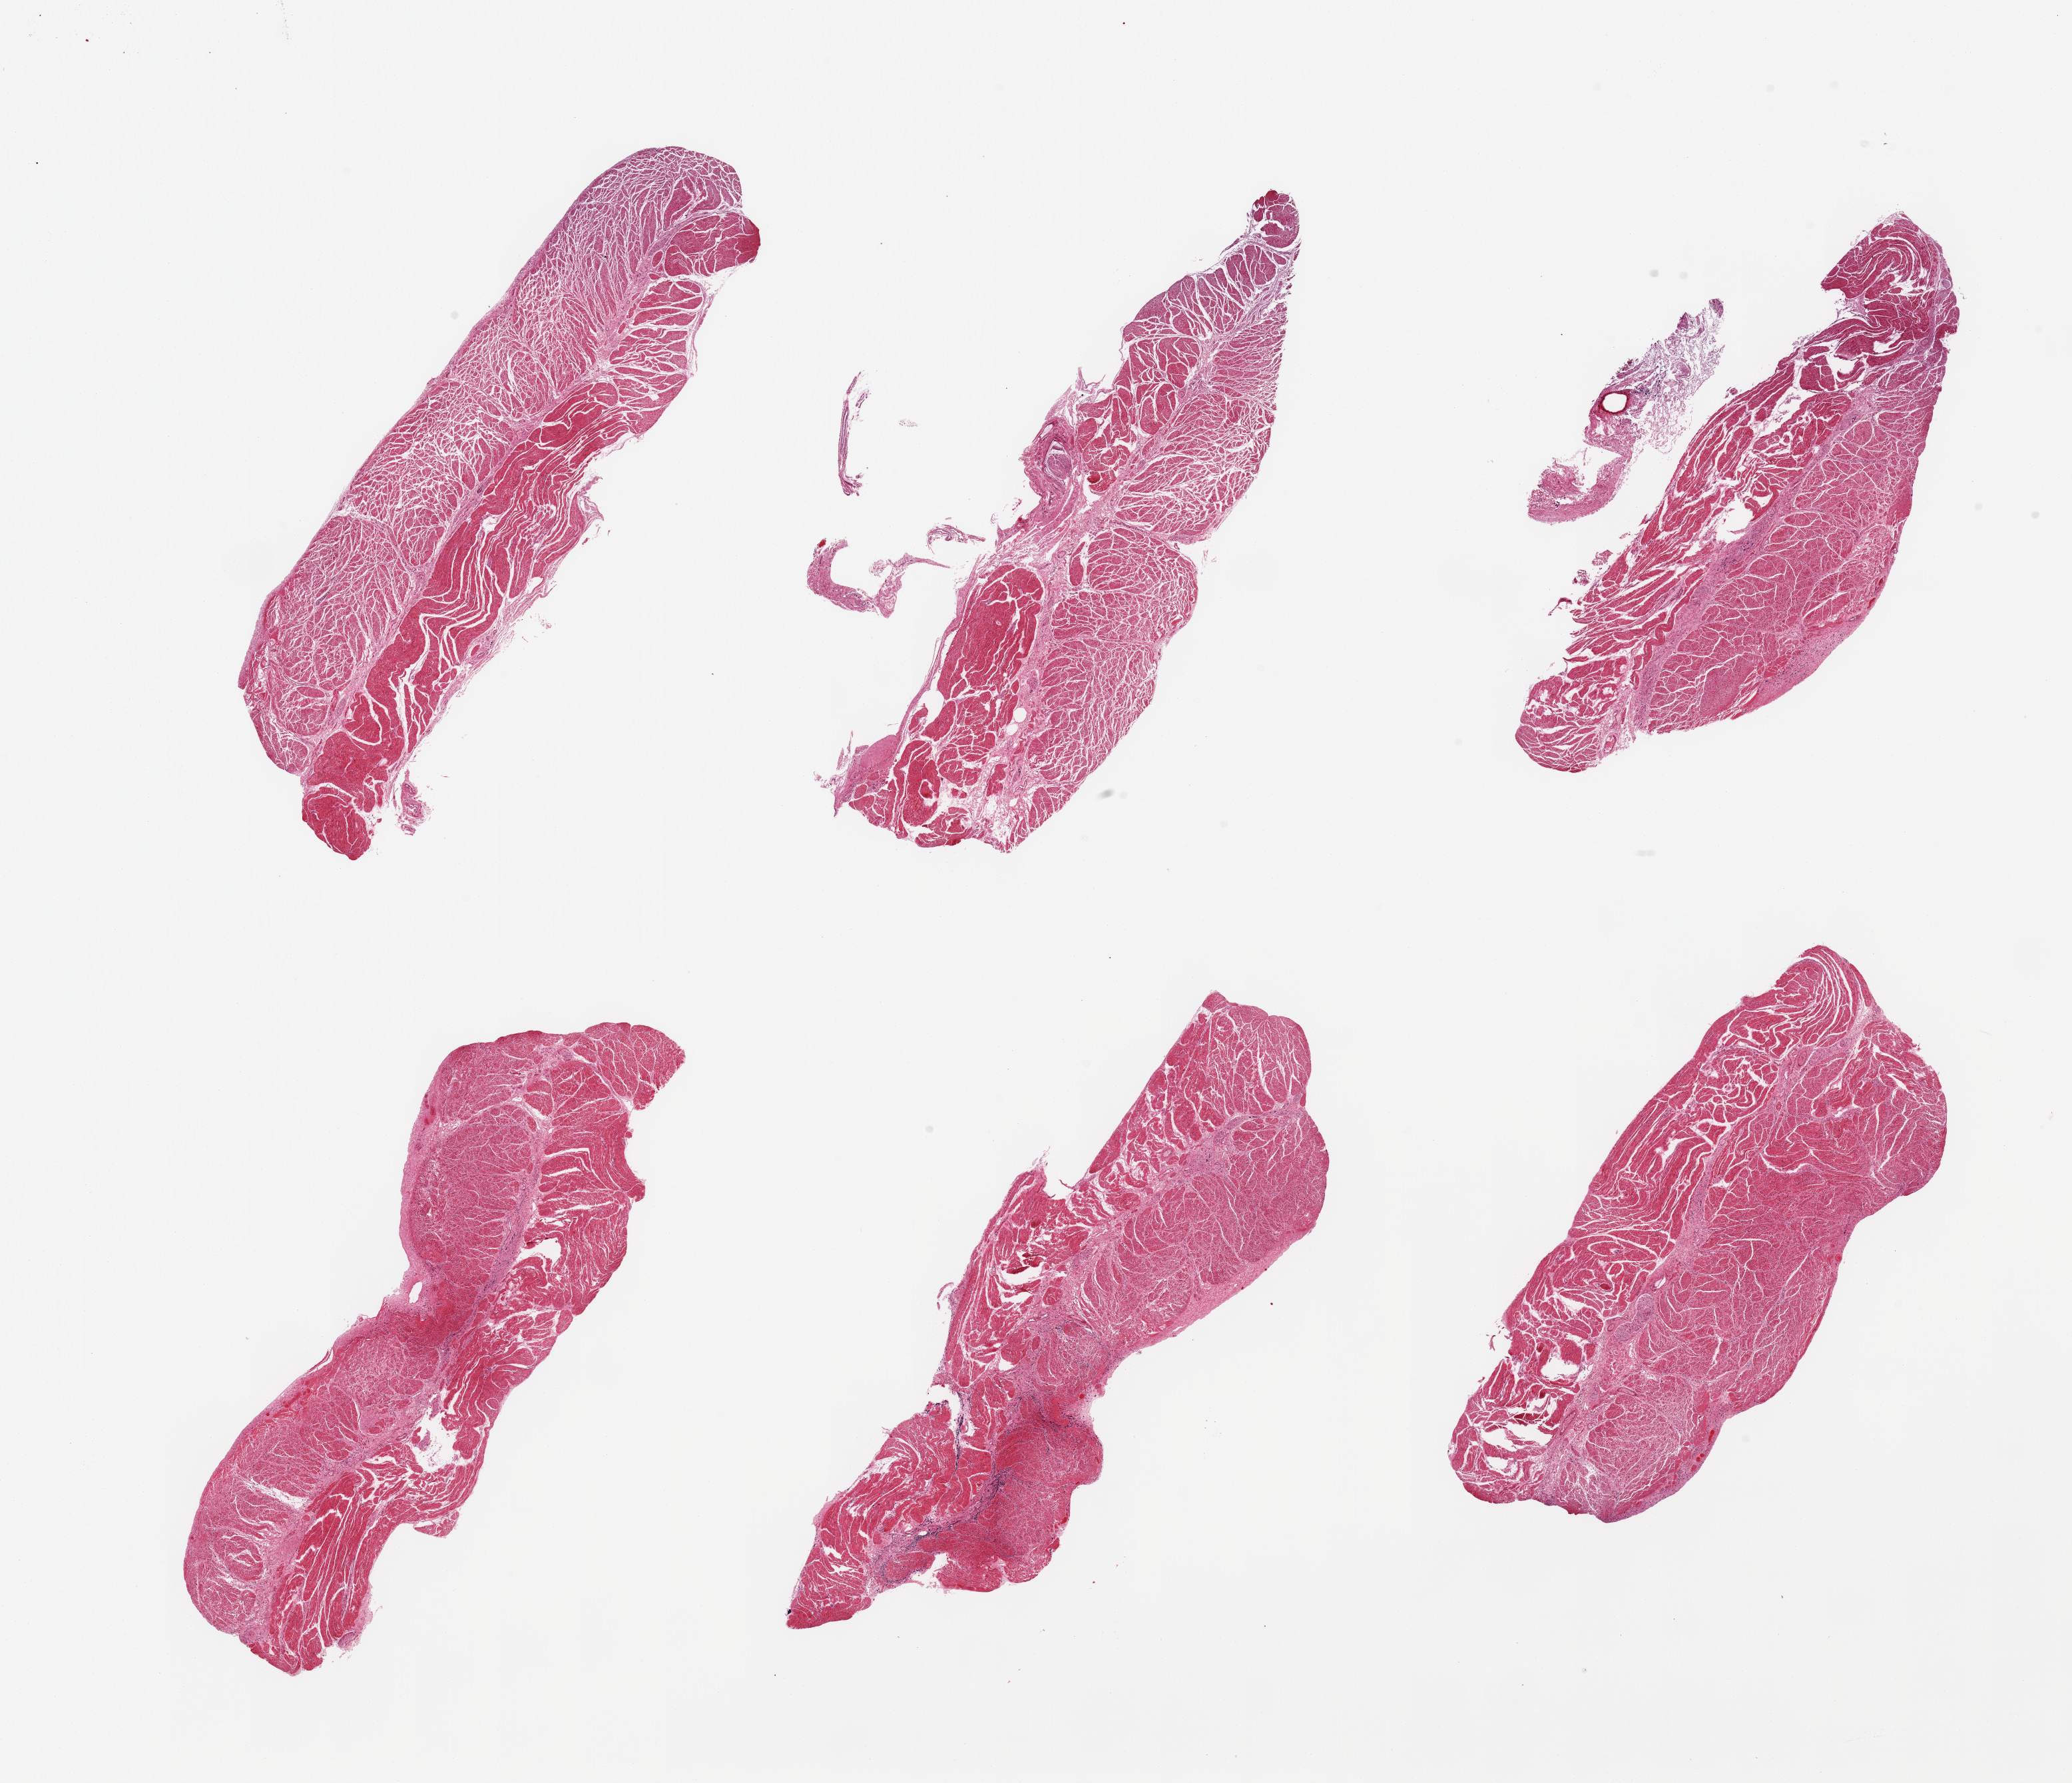
Whole-slide image, hematoxylin and eosin (H&E) stain, brightfield — shown as a low-resolution overview of the whole scanned area (about 24.6 x 21.2 mm), PAXgene-fixed paraffin-embedded (PFPE) section, target tissue: esophageal muscle, donor tissue sample.
Review note (as recorded): 6 pieces, confirmed target muscularis.